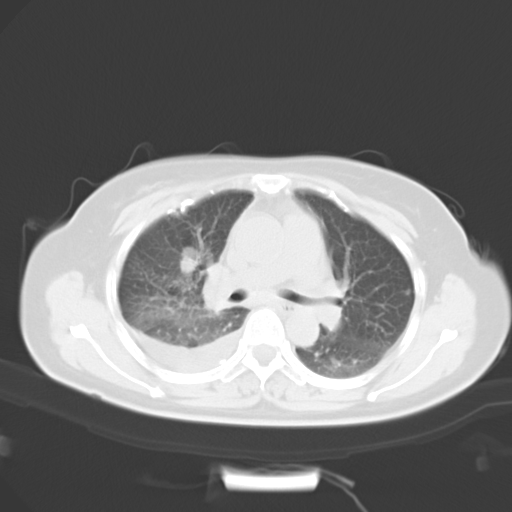
Chest CT, one axial slice. Slice 11 of 20 in the series (ordered by position). Reconstruction kernel B40f. 120 kVp. Lung window (W 1500 / L -600 HU). 512 × 512 image matrix. Female patient, age 53 years. Case-level facts recorded for this patient, not image findings: clinical TNM (as recorded): T1c N1 M1b.
Structures marked on this image (rectangle marked by the reading radiologist):
- lung tumour (recorded histology: adenocarcinoma): bounding box (x1, y1, x2, y2) in pixels: (176, 253, 198, 276)